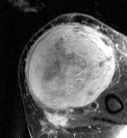
MRI of an extremity soft-tissue mass, one axial slice; position 31 of 87 along the scan axis; T2-weighted fat-saturated; MR volume resampled by the dataset authors to the PET/CT grid (not the native acquisition matrix); 3.27 mm slice thickness; 127 × 138 image matrix. Female patient. From the clinical record (not read from this slice): histological type: pleiomorphic leiomyosarcoma; grade: high; site of the primary tumour: left biceps.
Structures marked on this image (expert contour drawn on MRI and transferred to this co-registered scan by the dataset authors):
- gross tumour volume including surrounding oedema: bounding box [x1, y1, x2, y2] px = [24, 23, 115, 113]
- gross tumour volume (mass): [24, 23, 115, 111]